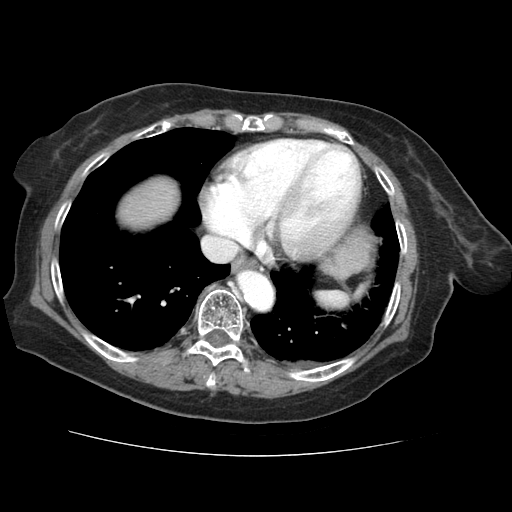
Contrast-enhanced abdominal CT (liver protocol), one axial slice. Position 62 of 73 along the scan axis. Soft-tissue window (W 400 / L 40 HU). 2.5 mm slice thickness. 512 × 512 image matrix, field of view 360 × 360 mm. From the clinical record (not read from this slice): diagnosis: hepatocellular carcinoma (patient treated with transarterial chemoembolisation; whether this scan precedes or follows treatment is not stated here); TNM stage (as recorded): Stage-IVB; Child-Pugh class: A; tumour nodularity: uninodular.
Structures marked on this image (semi-automatically segmented with operator editing):
- liver parenchyma outside the tumour (the mass and vessels are separate outlines, so this box may not span the whole liver): bounding box (x1, y1, x2, y2) in pixels: (120, 180, 176, 226)